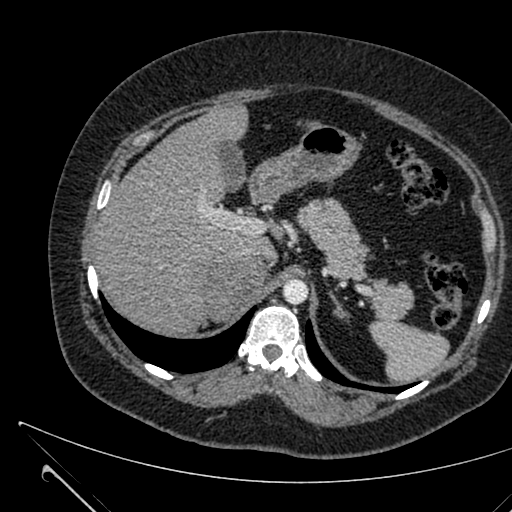
Contrast-enhanced abdominal CT, one axial slice. Position 467 of 731 along the scan axis. 120 kVp. Intravenous contrast given. Soft-tissue window (W 400 / L 40 HU). 512 × 512 image matrix, field of view 376 × 376 mm. Patient: female, 36 years. From the clinical record (not read from this slice): diagnosis: adrenocortical carcinoma; tumour side: right adrenal; tumour size at pathology: 10 cm; Ki-67 index: 20 %; stage (as recorded): 4.
Annotated regions visible in this slice (semi-automatic segmentation, software-assisted and operator-edited):
- mass: bounding box <206,257,267,319> (left, top, right, bottom; pixels)